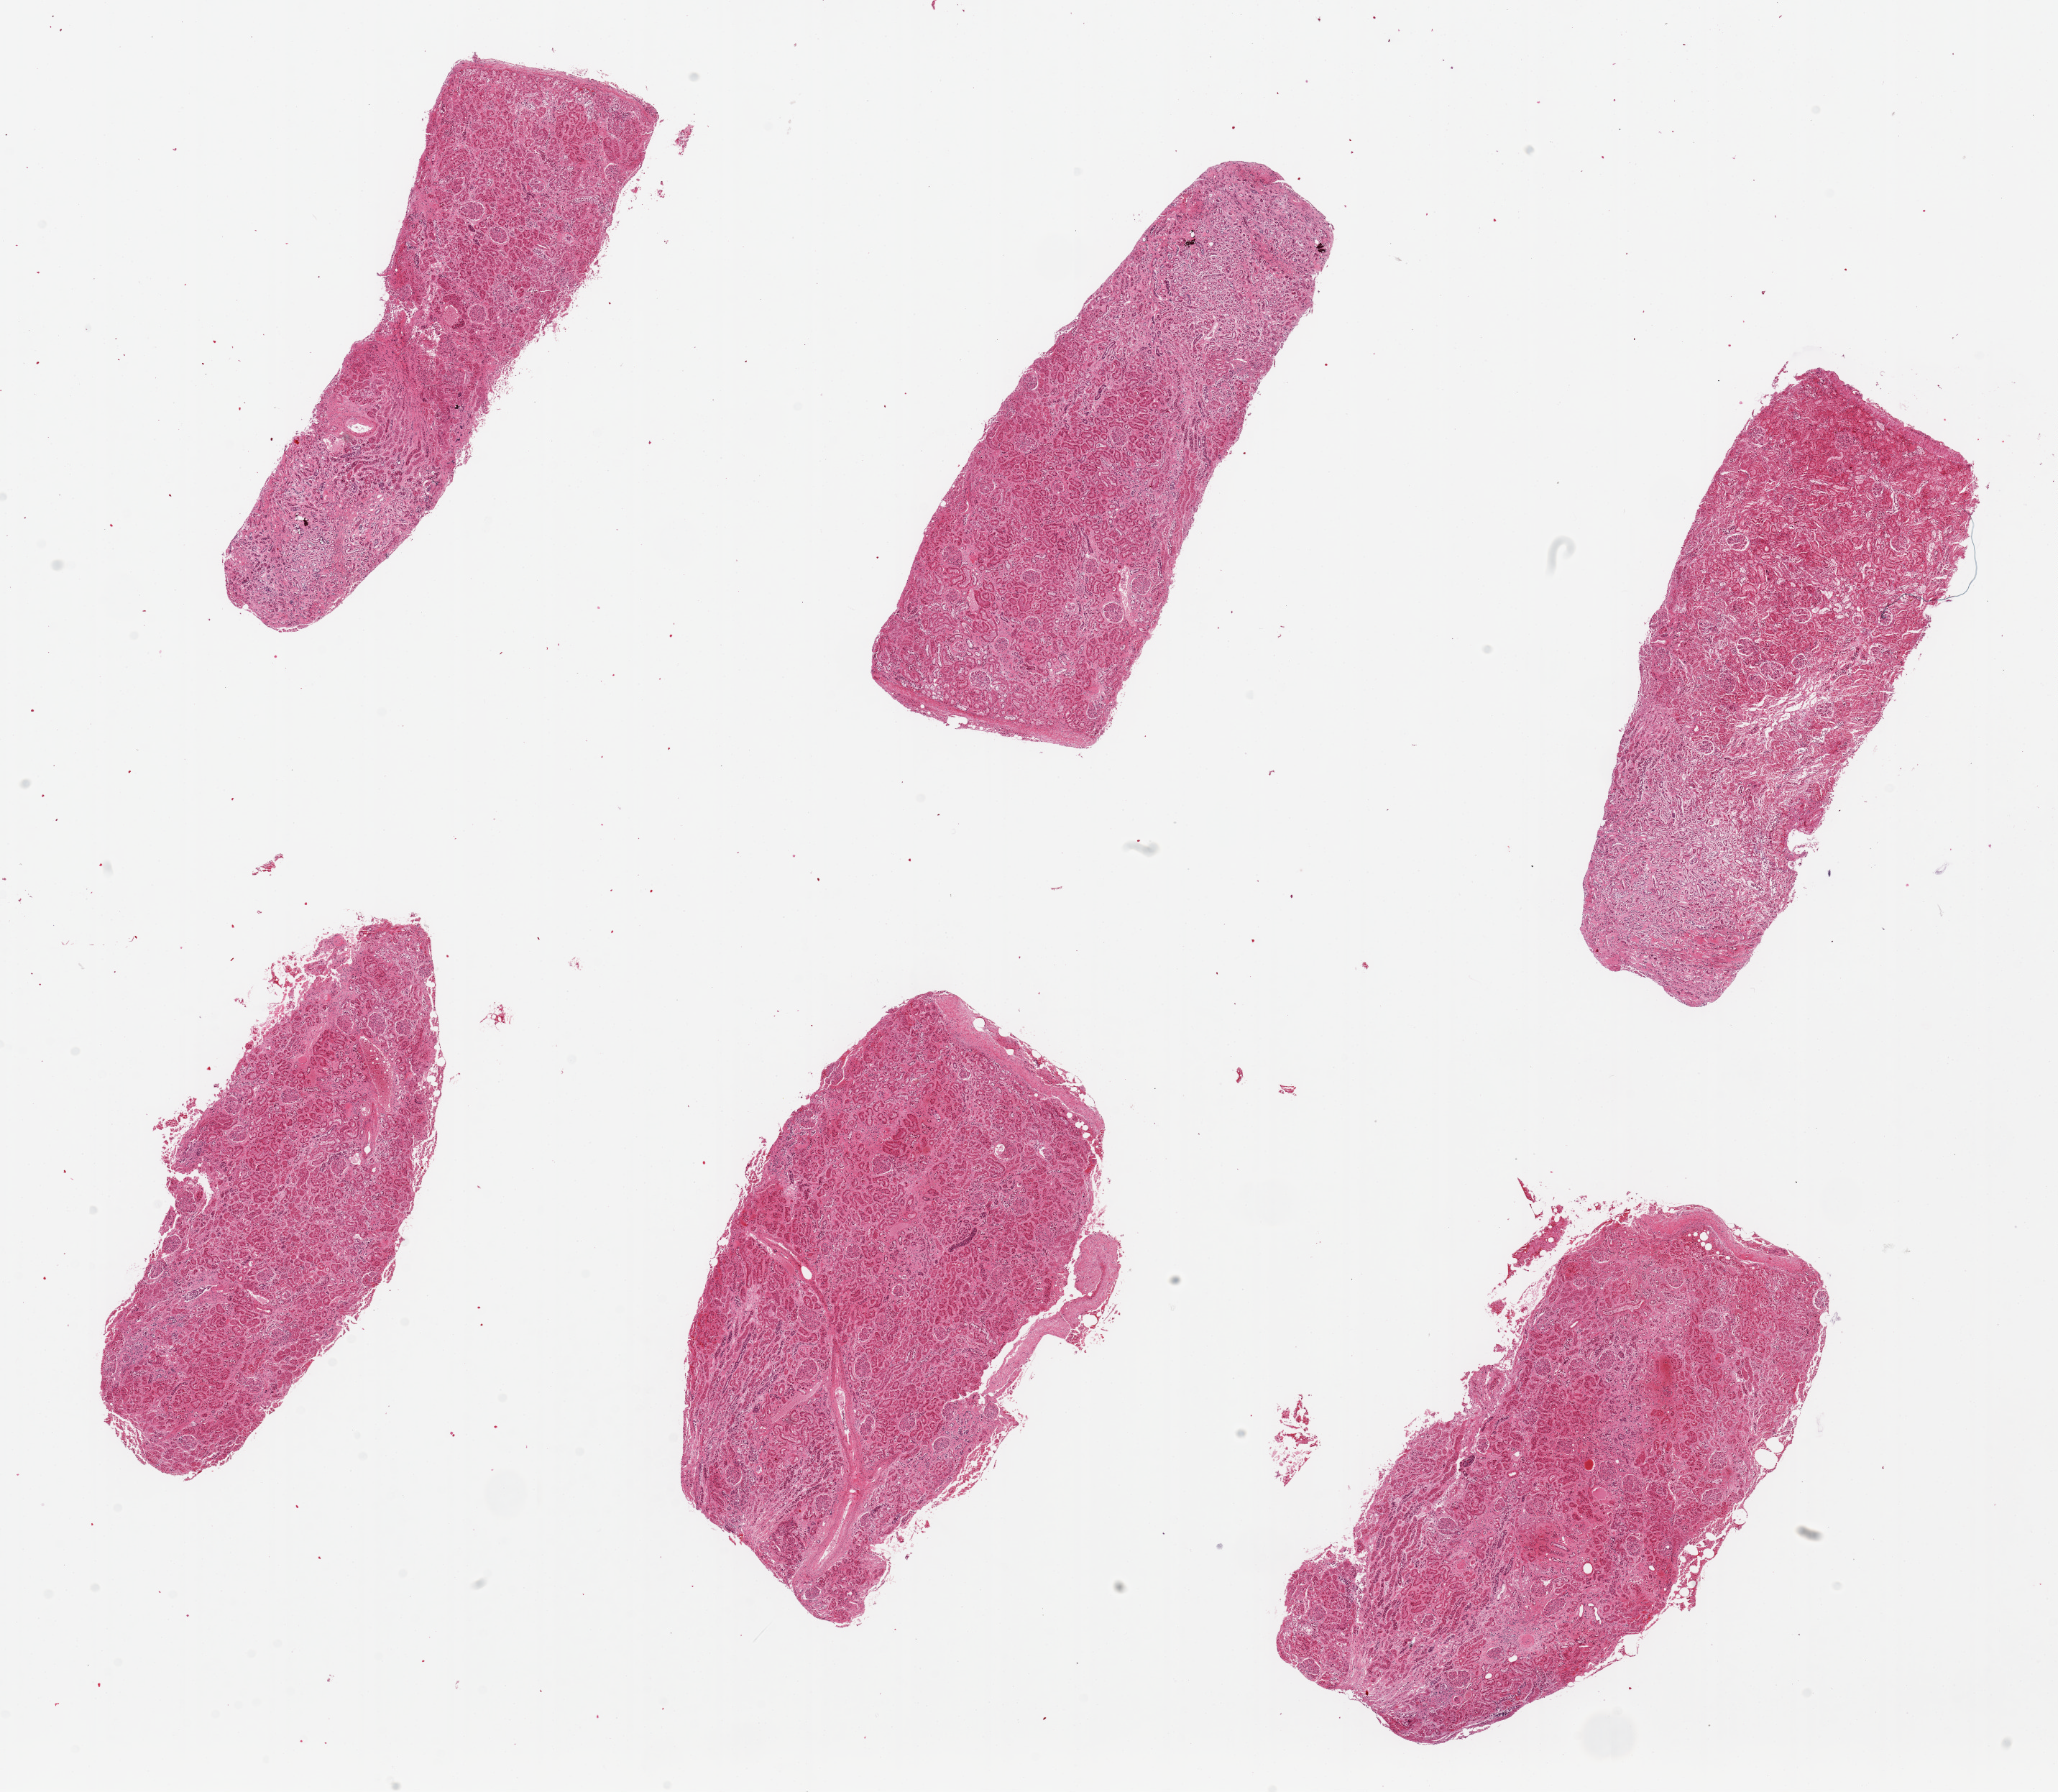
Digitized haematoxylin and eosin-stained section, whole scanned area (about 22.6 x 19.7 mm) shown as a low-resolution overview. PAXgene-fixed paraffin-embedded (PFPE) section. Section of renal cortex (target tissue). Donor tissue sample.
Pathologist's review note for this sample: 6 pieces. up to 7x3mm; tubules 2-3; all cortex; no notable chronic glomerular or vascular lesions.